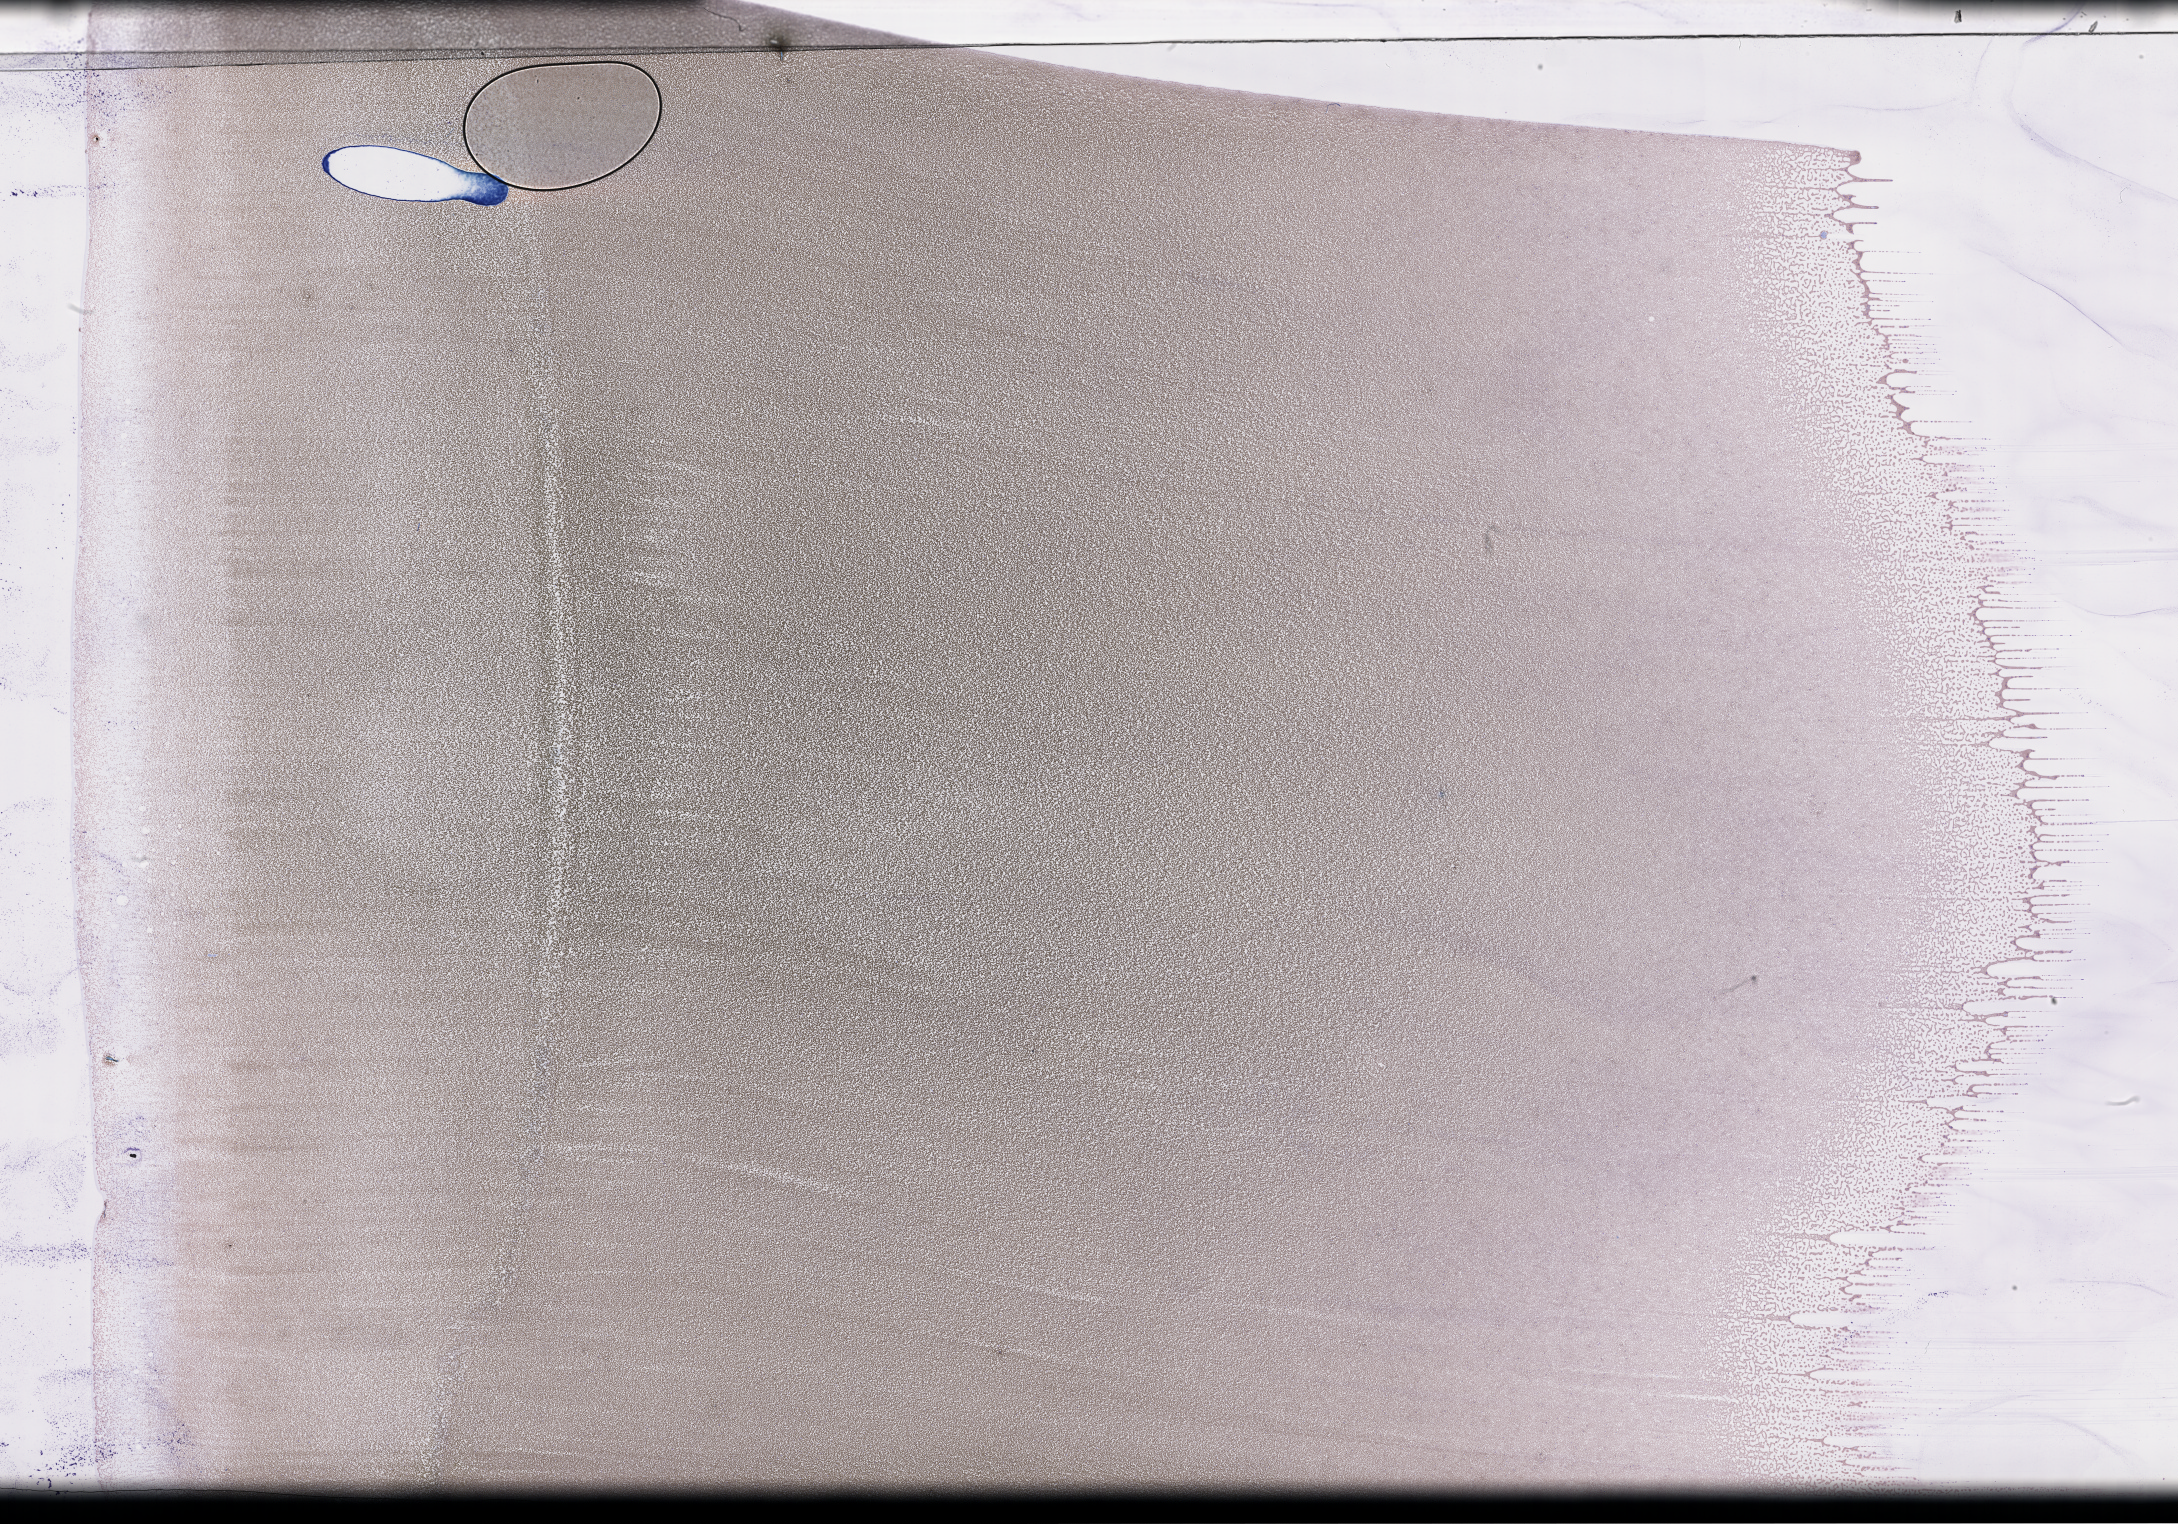
Wright–Giemsa-stained whole blood smear, whole-slide image, whole scanned area (about 35.2 x 24.6 mm) shown as a low-resolution overview; EDTA-anticoagulated smear; specimen time point: collected on treatment. Patient: female.
From a patient with: Plasma Cell Myeloma.